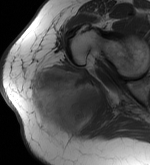
MRI of an extremity soft-tissue mass, one axial slice. Position 36 of 56 along the scan axis. MR volume resampled by the dataset authors to the PET/CT grid (not the native acquisition matrix). 3.27 mm slice thickness. 150 × 165 image matrix, field of view 146 × 161 mm. Female patient. Case-level facts recorded for this patient, not image findings: histological type: epithelioid sarcoma with vascular differentiation; site of the primary tumour: right buttock.
Outlined on this slice (expert contour drawn on MRI and transferred to this co-registered scan by the dataset authors):
- gross tumour volume (mass): bounding box <28,67,113,130> (left, top, right, bottom; pixels)